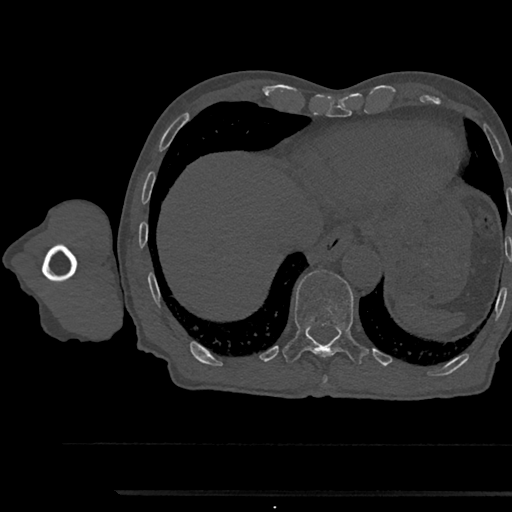
CT including the spine, one axial slice. Slice 795 of 797 in the series (ordered by position). Reconstruction kernel Br40s/3. 120 kVp. Bone window (W 1800 / L 400 HU). 0.5 mm slice thickness. 512 × 512 image matrix, field of view 367 × 367 mm. Patient: male, 79 years. From the clinical record (not read from this slice): primary cancer: prostate.
Annotated regions visible in this slice (semi-automatically segmented with operator editing):
- T11 vertebra: box from (x=282, y=271) to (x=368, y=362) px